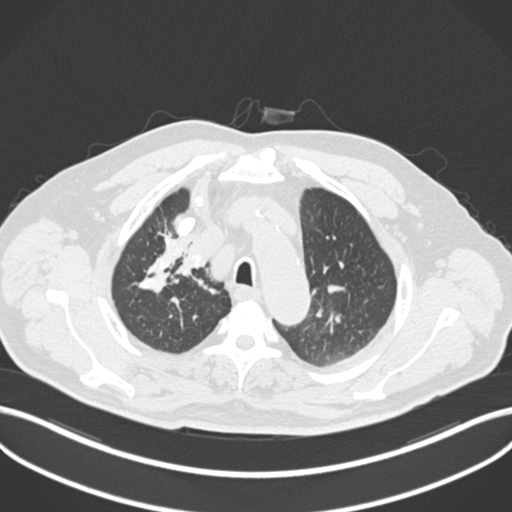
Chest CT, one axial slice; position 160 of 255 along the scan axis; reconstruction kernel B30f; 120 kVp; lung window (W 1500 / L -600 HU); 512 × 512 image matrix, field of view 400 × 400 mm. Patient: male, 60 years. From the clinical record (not read from this slice): clinical TNM (as recorded): T1b N1 M0.
Annotated regions visible in this slice (rectangle marked by the reading radiologist):
- lung tumour (recorded histology: squamous cell carcinoma): box from (x=165, y=245) to (x=211, y=285) px